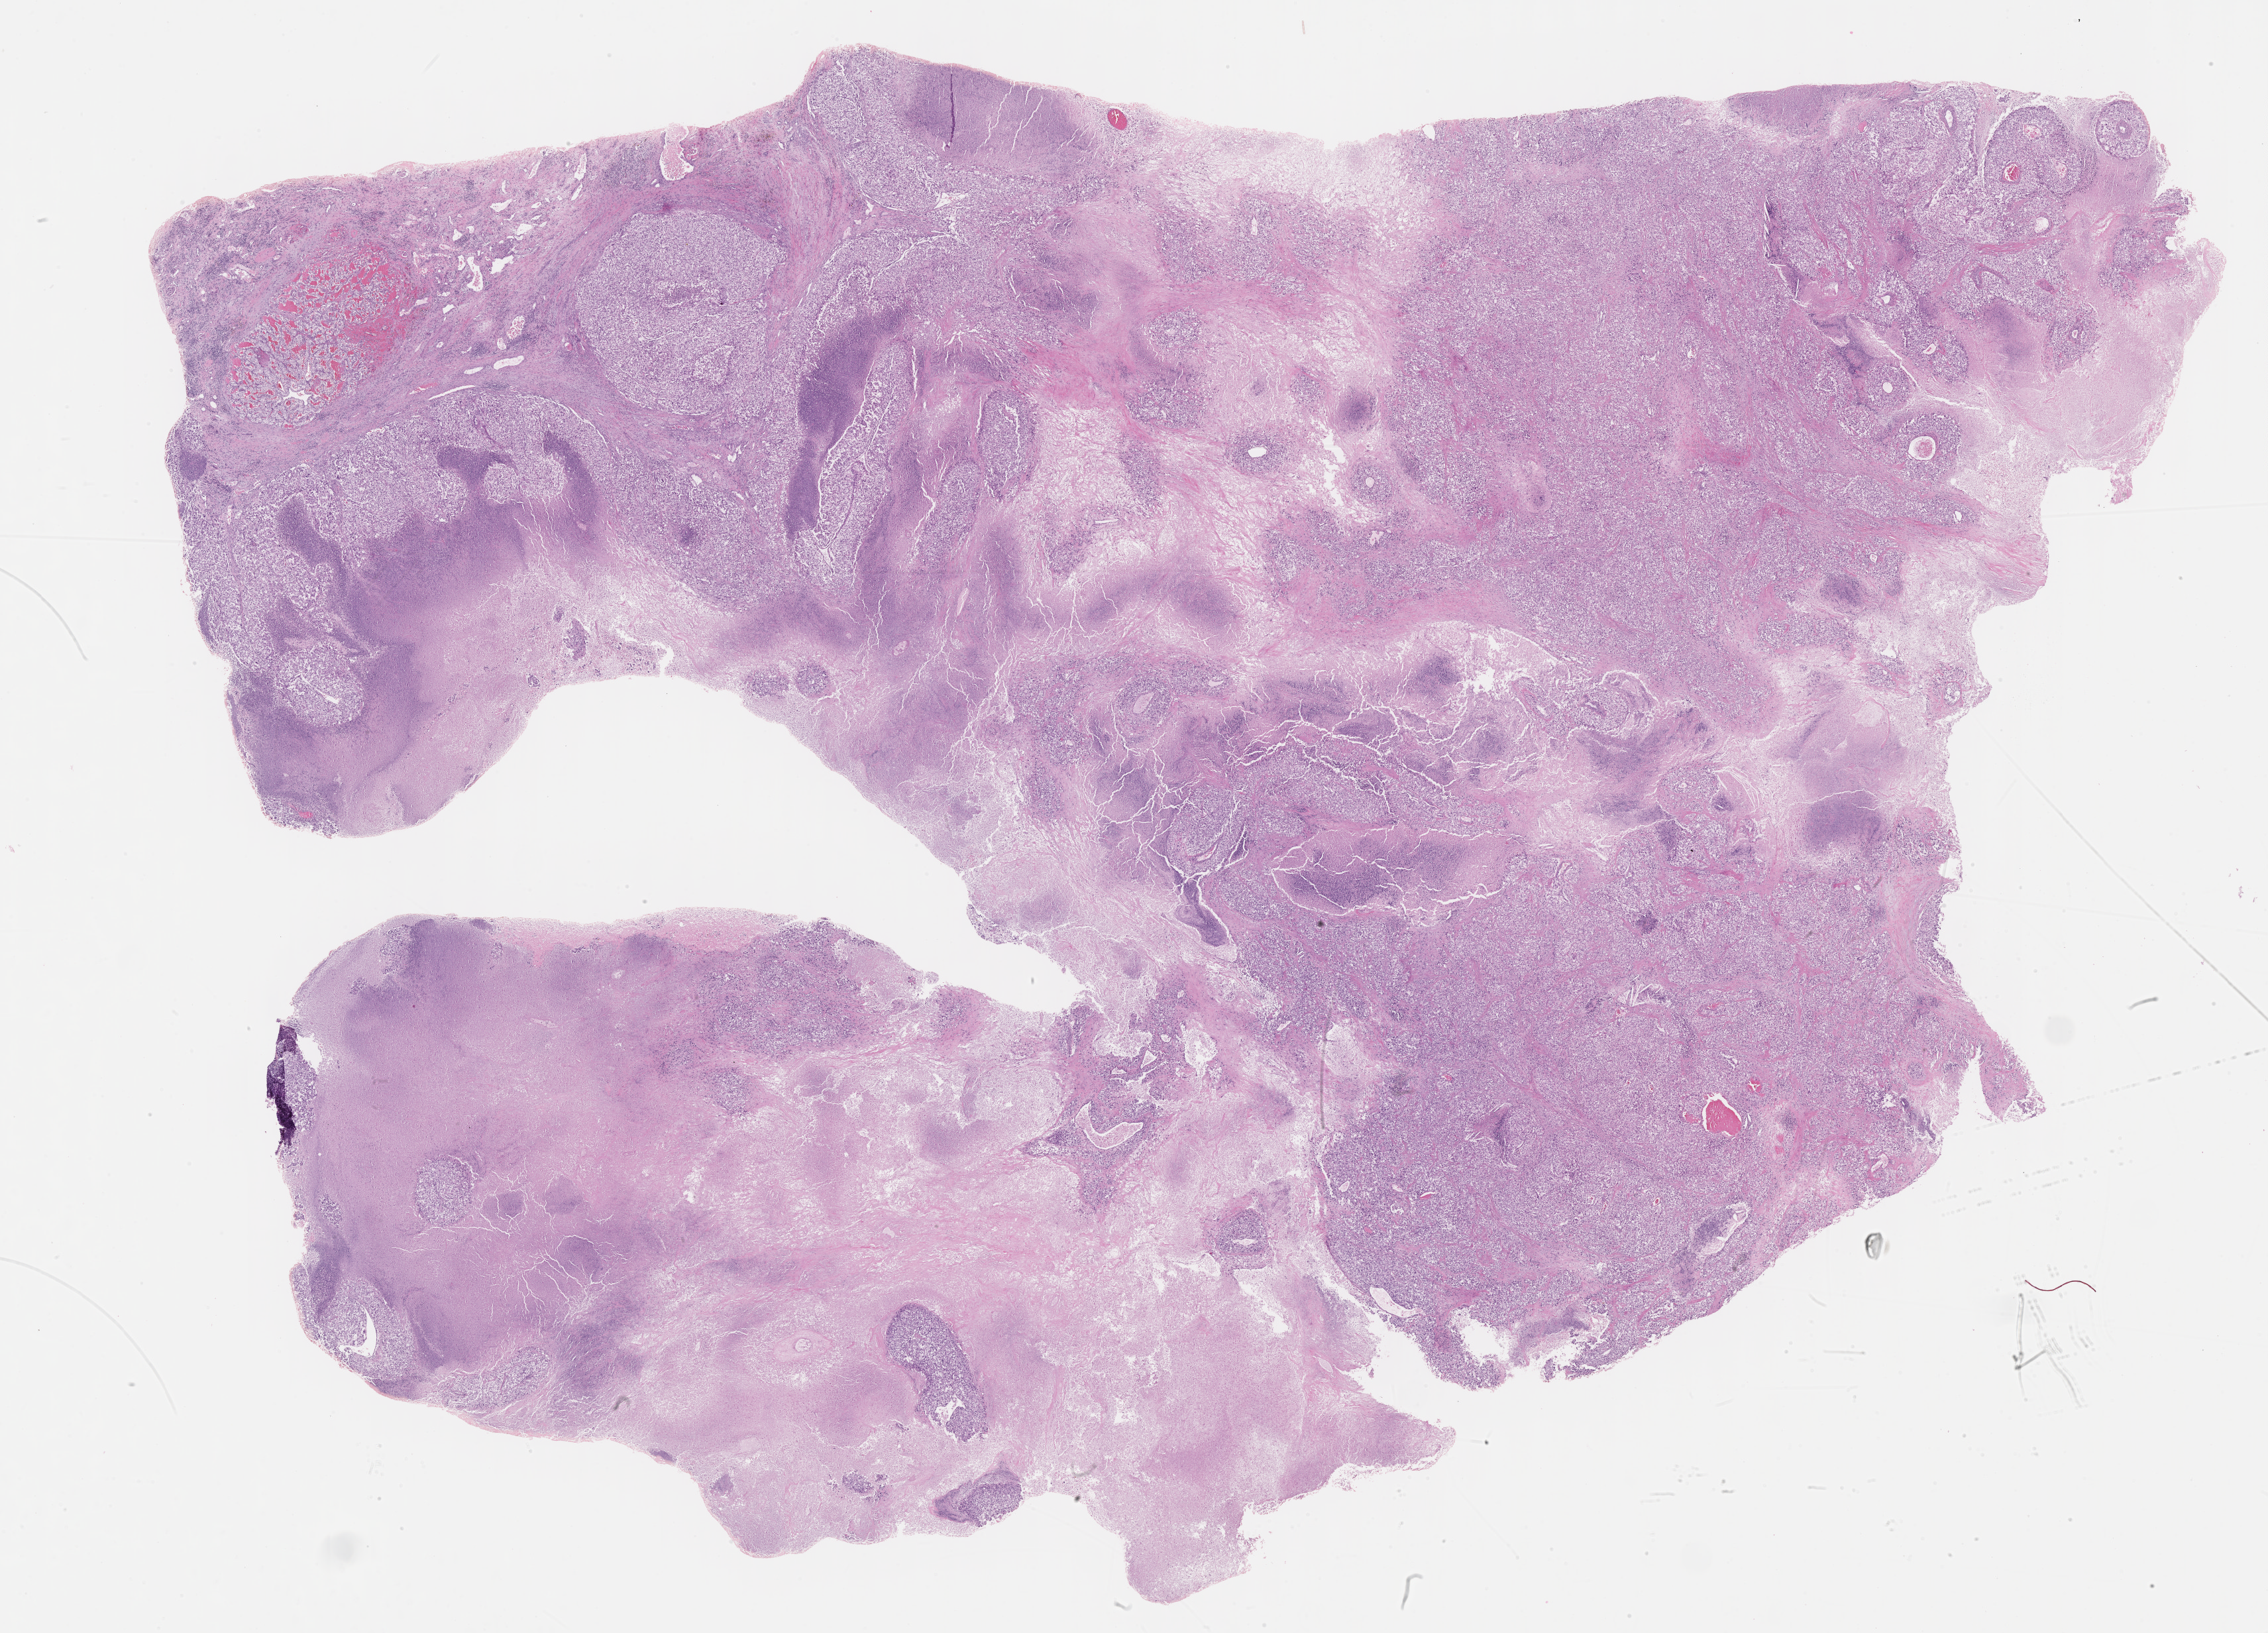
Whole-slide histology image, H&E — shown as a low-resolution overview of the whole scanned area (about 27.7 x 19.9 mm); formalin-fixed paraffin-embedded (FFPE) diagnostic section; kidney, primary tumour sample. Male patient; age at initial diagnosis 72 years.
Histologic diagnosis: Clear cell adenocarcinoma, NOS.